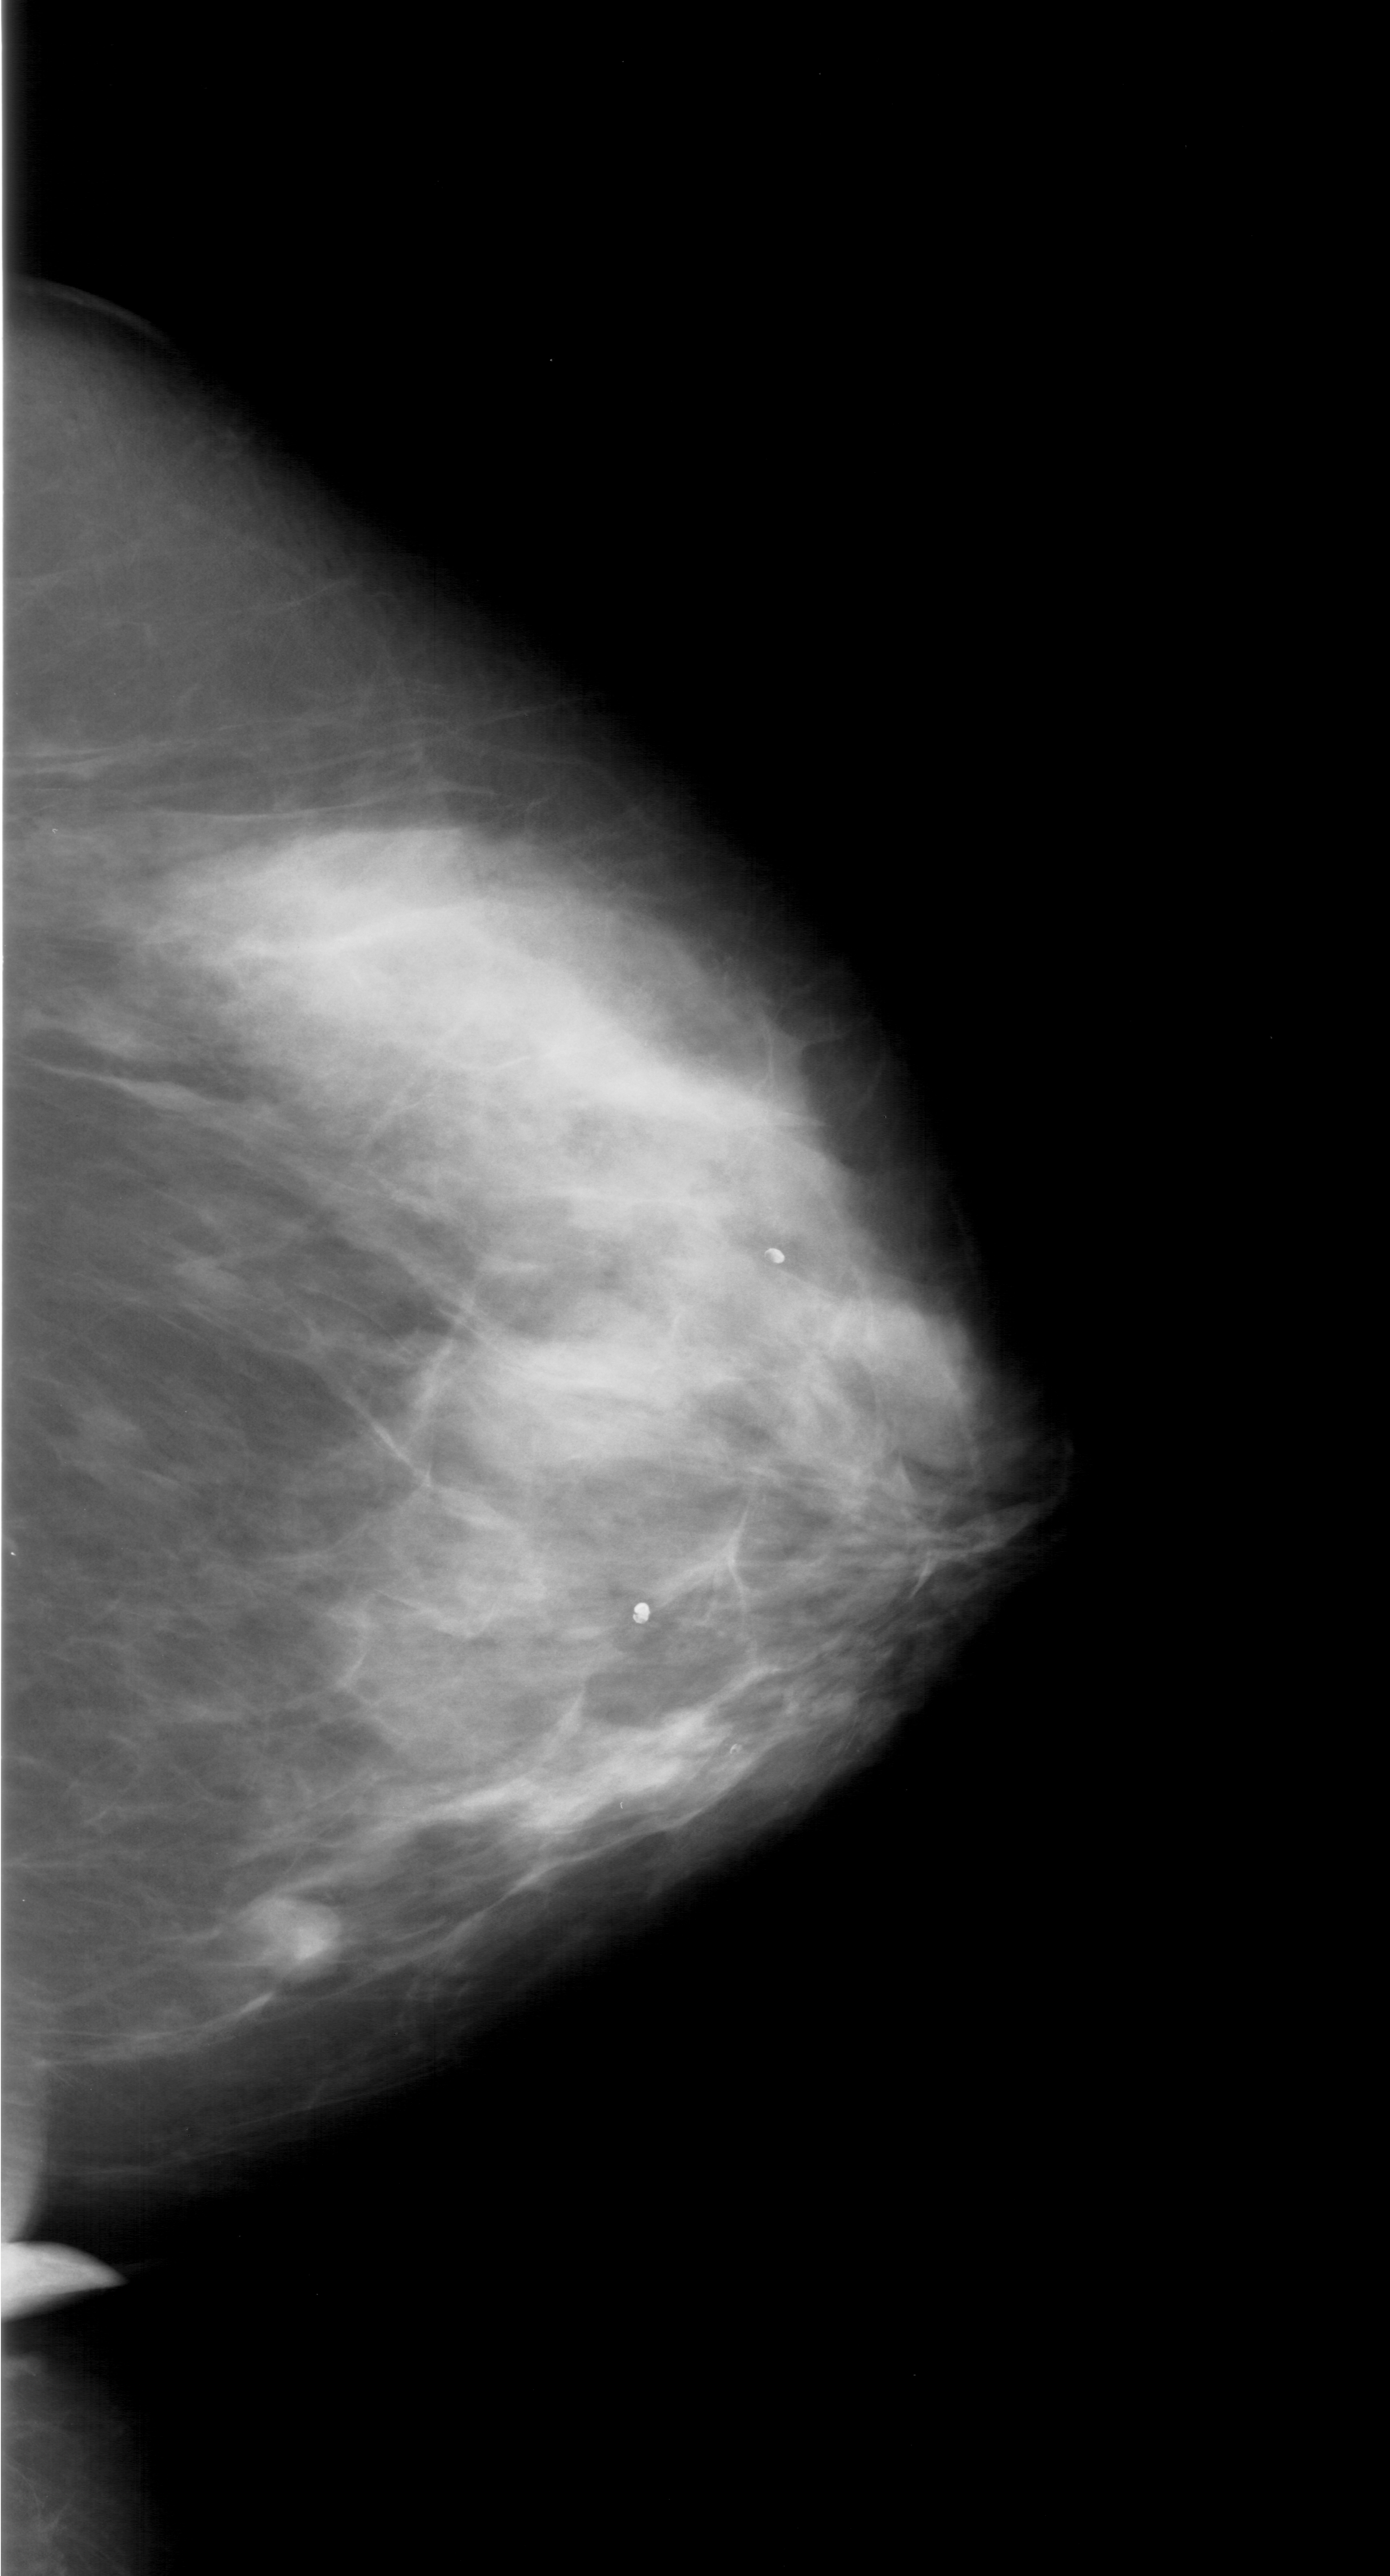
Scanned film-screen mammogram, right breast, CC view, BI-RADS breast density category 4 (scale 1–4).
- Mass, shape lobulated, margins ill defined; BI-RADS assessment category 4; pathology result (as recorded, not read from the image): malignant.